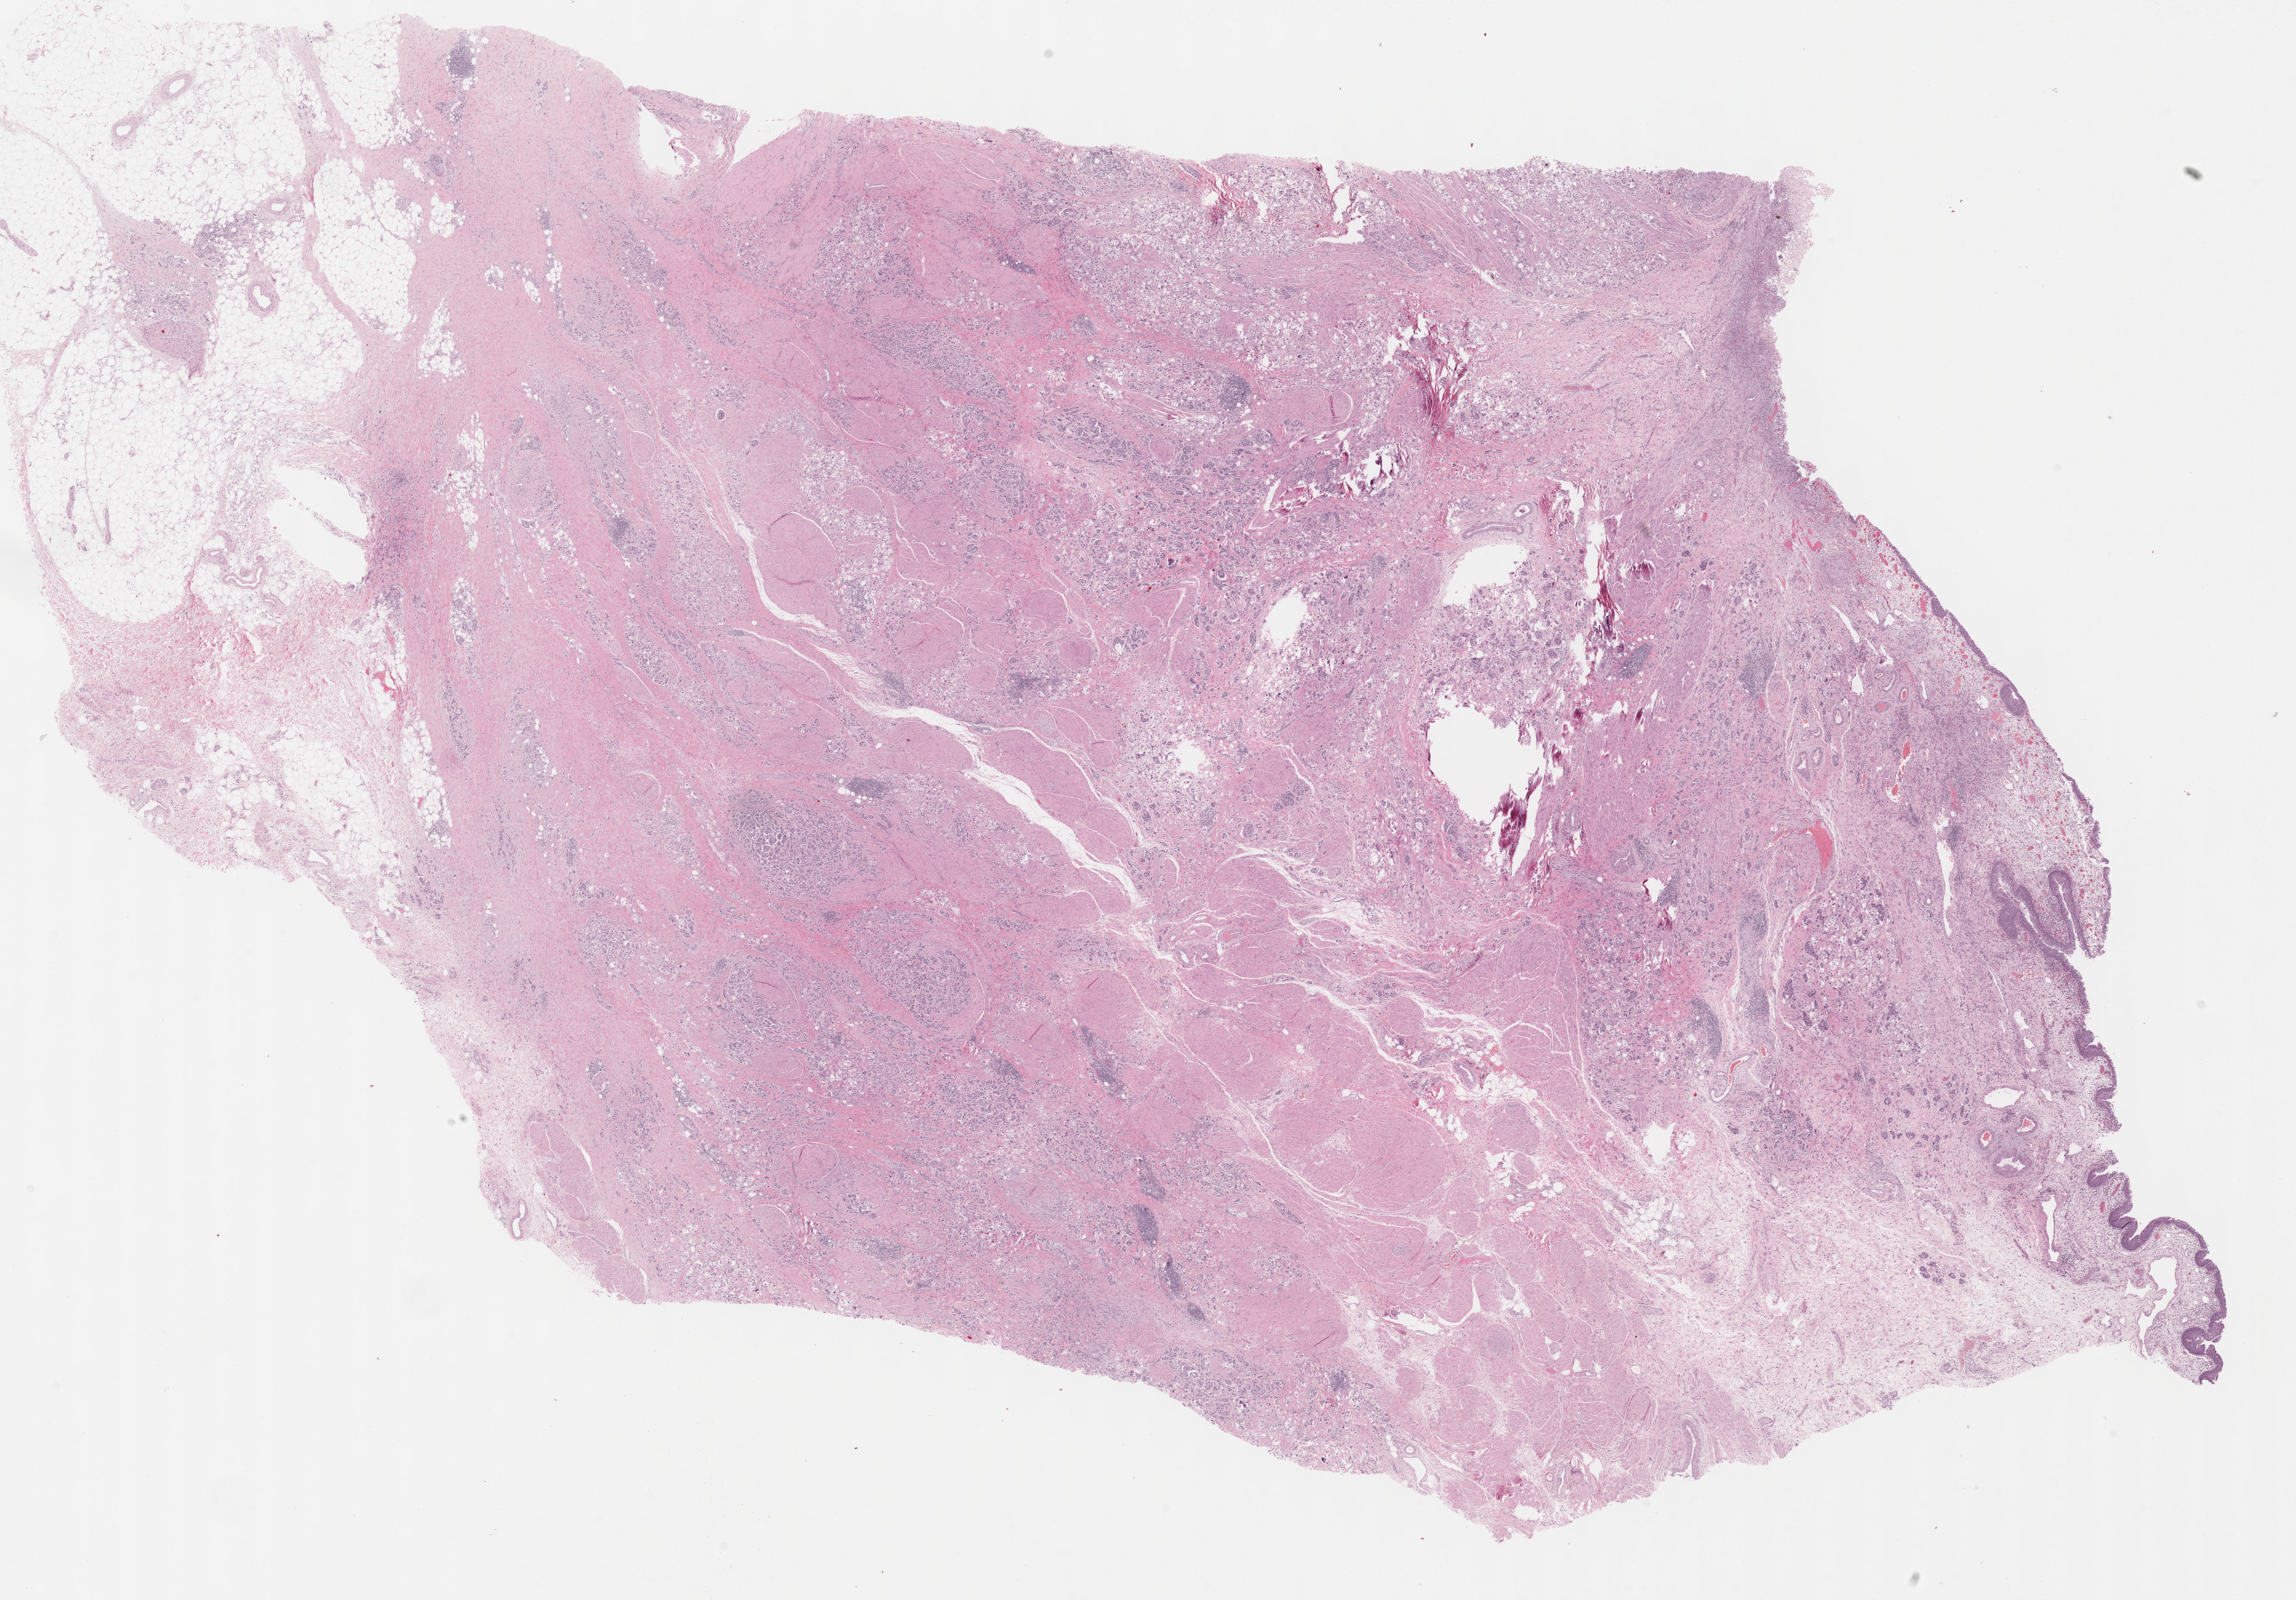
Whole-slide histology image, H&E-stained, shown as a low-resolution overview of the whole scanned area (about 25.2 x 17.5 mm). Formalin-fixed paraffin-embedded (FFPE) diagnostic section. Sample: primary tumour, bladder. Female, age 80 years at initial diagnosis. Histologic grade: high grade.
Lymph nodes positive (case pathology): 4 of 35 examined. Diagnosis: Transitional cell carcinoma. AJCC pathologic stage: IV.